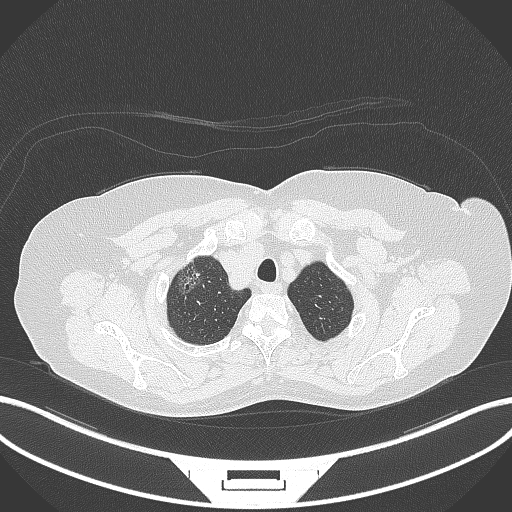
Chest CT, one axial slice; slice 312 of 365 in the series (ordered by position); 120 kVp; lung window (W 1500 / L -600 HU); 1 mm slice thickness; 512 × 512 image matrix, field of view 400 × 400 mm. Patient: female, 62 years. From the clinical record (not read from this slice): clinical TNM (as recorded): T1c N0 M0.
Annotated regions visible in this slice (bounding box drawn by a radiologist):
- lung tumour (recorded histology: adenocarcinoma): bounding box (x1, y1, x2, y2) in pixels: (173, 255, 208, 300)